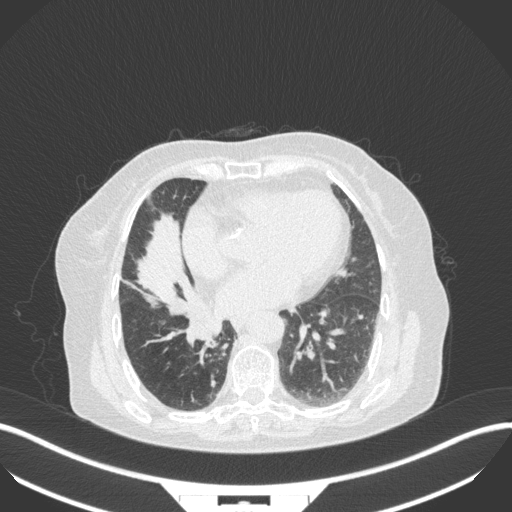
Chest CT, one axial slice. Slice 124 of 329 in the series (ordered by position). Reconstruction kernel B31f. 120 kVp. Lung window (W 1500 / L -600 HU). 1 mm slice thickness. 512 × 512 image matrix, field of view 400 × 400 mm. Female patient, age 75 years. From the clinical record (not read from this slice): clinical TNM (as recorded): T1b N0 M1a.
Outlined on this slice (rectangle marked by the reading radiologist):
- lung tumour (recorded histology: squamous cell carcinoma): bounding box (x1, y1, x2, y2) in pixels: (185, 311, 224, 346)